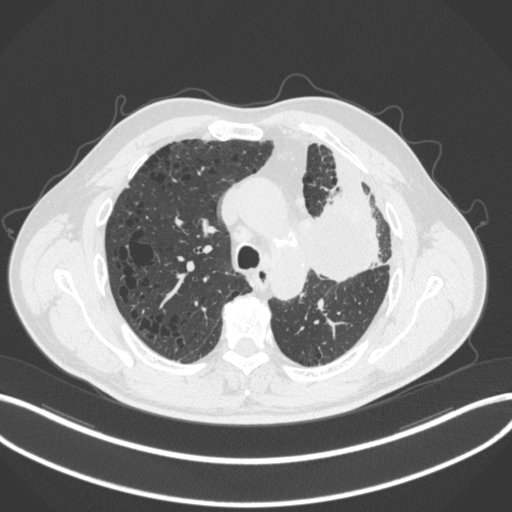
Chest CT, one axial slice. Position 205 of 286 along the scan axis. 120 kVp. Lung window (W 1500 / L -600 HU). 1 mm slice thickness. 512 × 512 image matrix, field of view 400 × 400 mm. Patient: male, 68 years. Case-level facts recorded for this patient, not image findings: clinical TNM (as recorded): T3 N3 M1.
Structures marked on this image (rectangle marked by the reading radiologist):
- lung tumour (recorded histology: adenocarcinoma): bounding box [x1, y1, x2, y2] px = [311, 175, 384, 287]